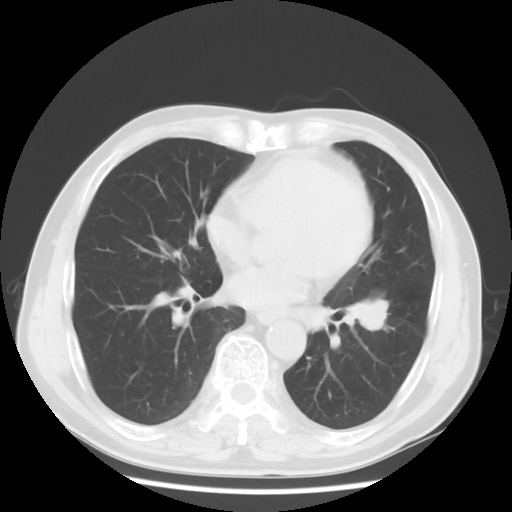
Chest CT, one axial slice; position 29 of 68 along the scan axis; lung window (W 1500 / L -600 HU); 5 mm slice thickness; 512 × 512 image matrix, field of view 360 × 360 mm. Male patient, age 71 years. From the clinical record (not read from this slice): clinical TNM (as recorded): T1c N1 M0; histopathological grade: G2-3.
Annotated regions visible in this slice (bounding box drawn by a radiologist):
- lung tumour (recorded histology: adenocarcinoma): box from (x=344, y=289) to (x=398, y=338) px